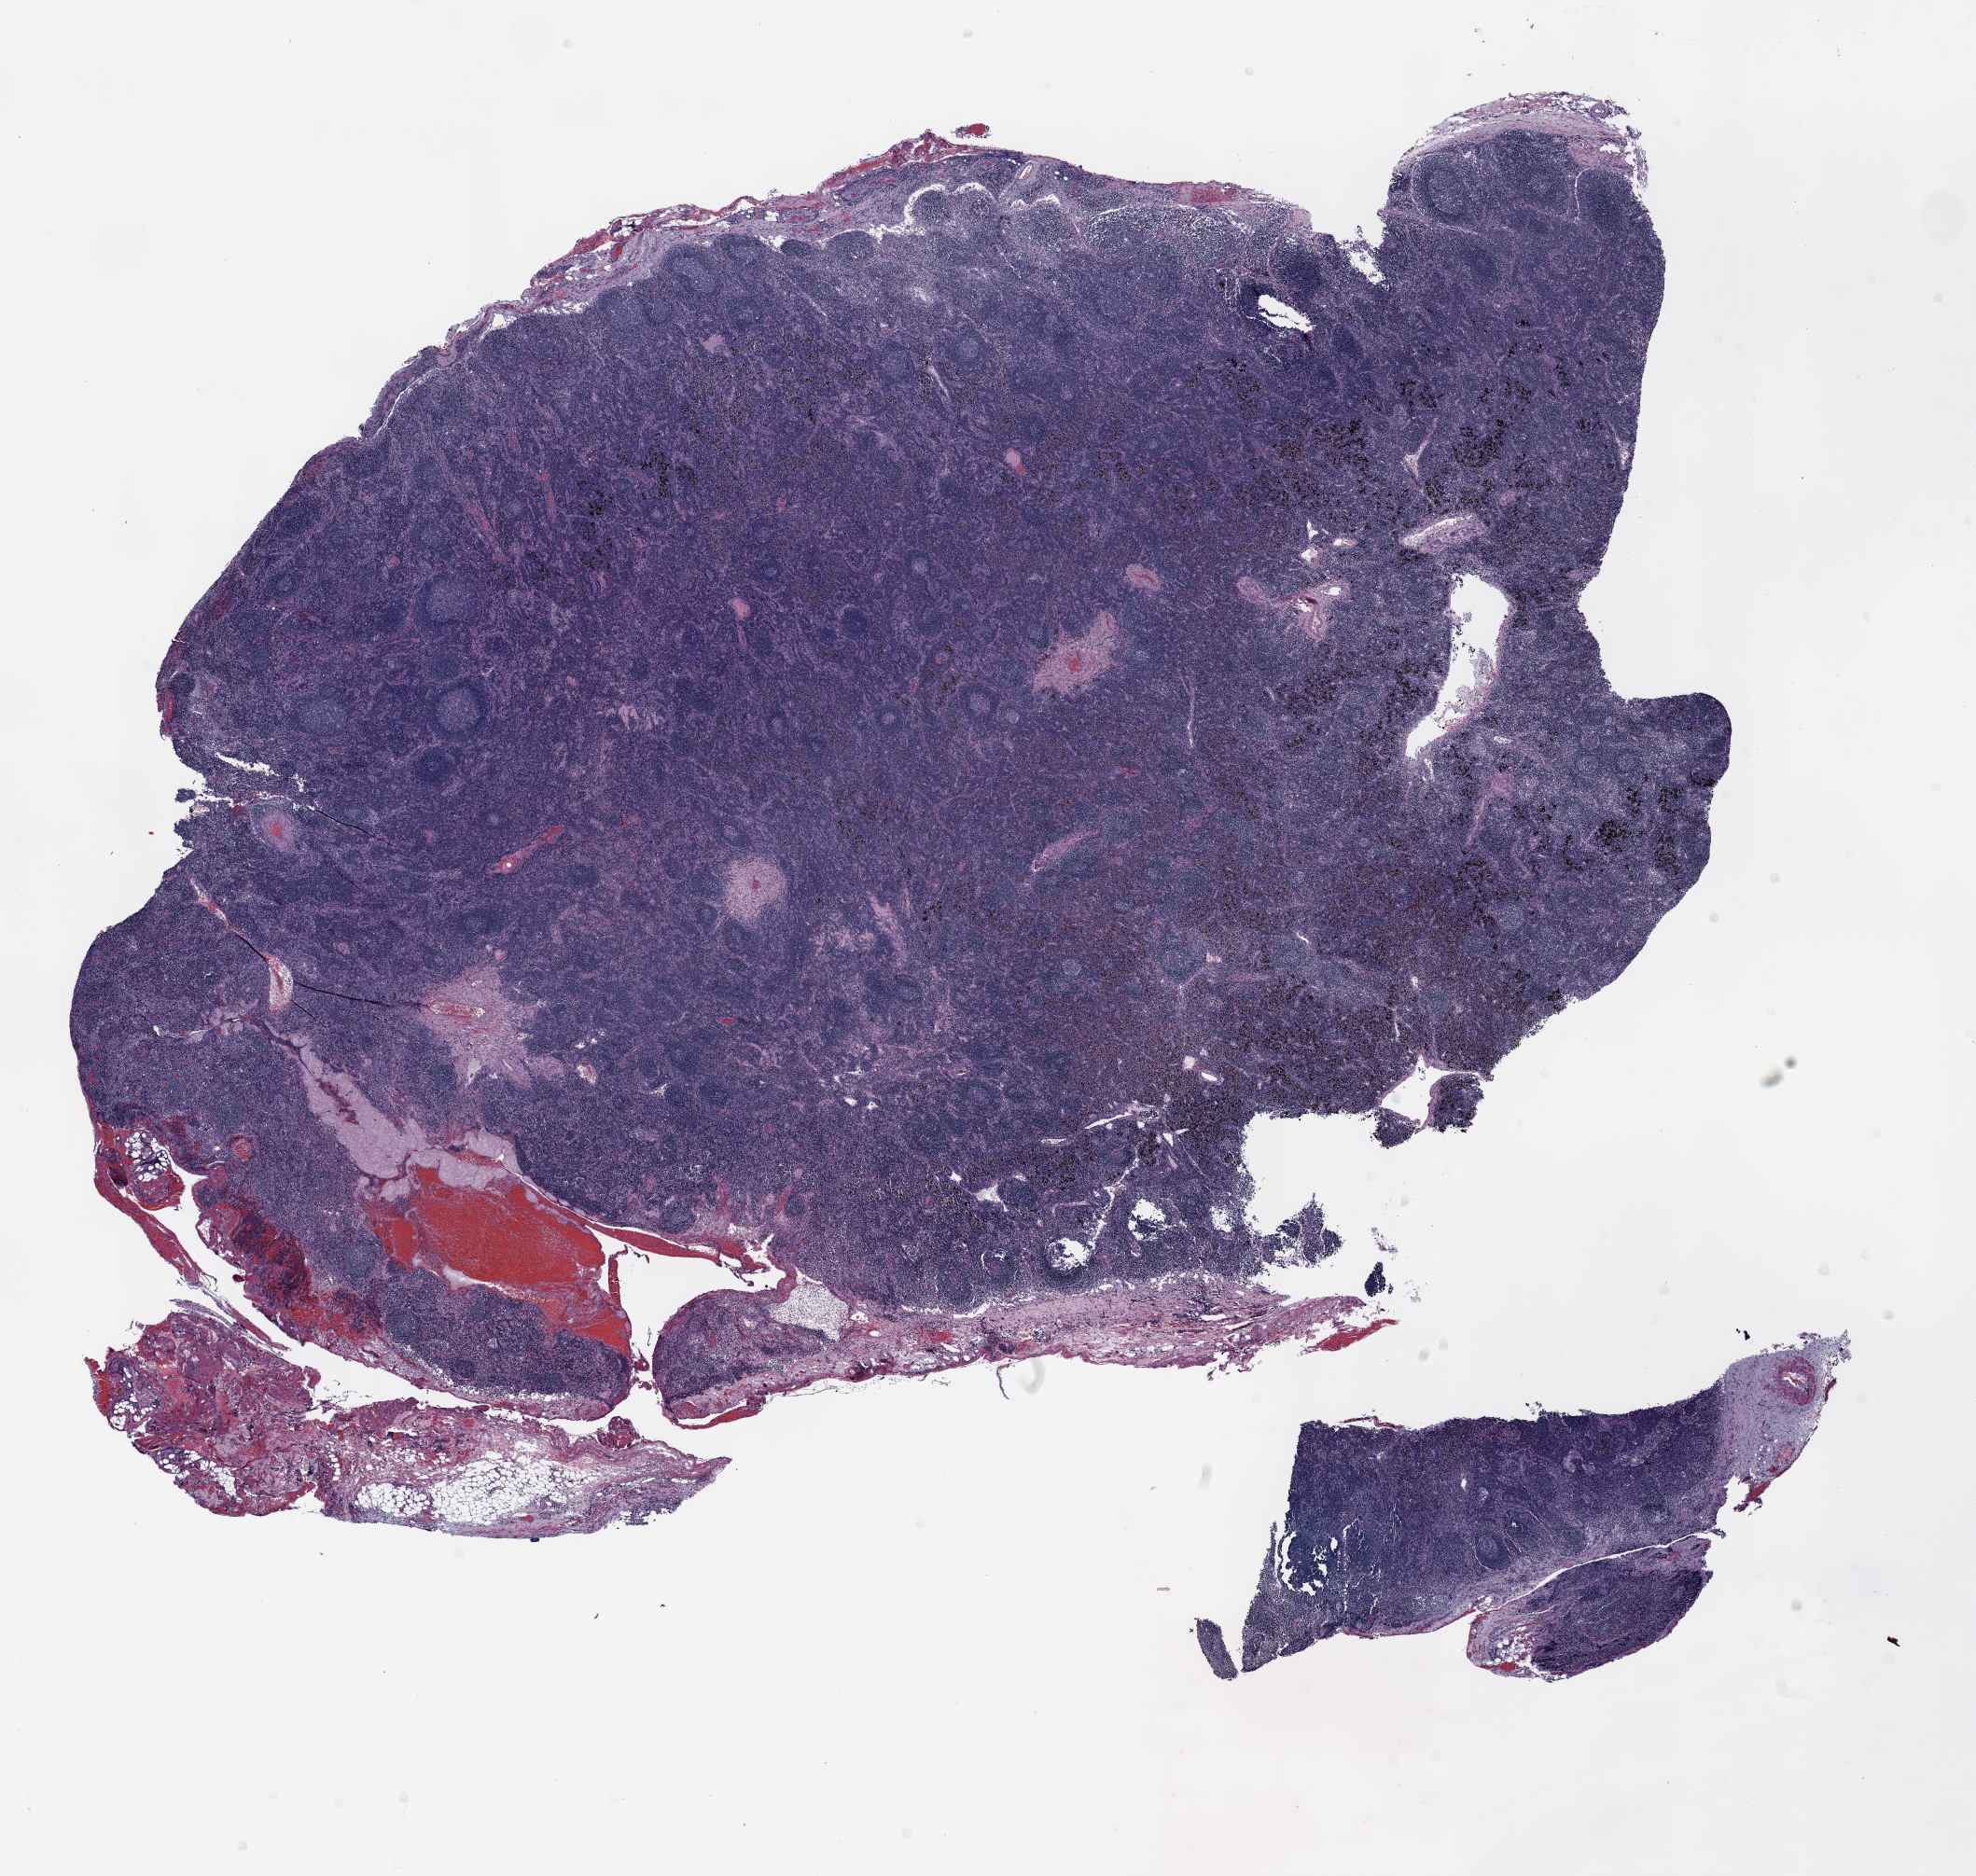
Whole-slide histology image, H&E — a low-resolution overview of the entire scanned area, about 17.0 x 16.2 mm (from a 20x scan). Formalin-fixed paraffin-embedded (FFPE) section. Lung. Male, age 55 at enrolment. Current smoker at enrolment. Grade: poorly differentiated (G3).
Primary tumour location (clinical record): right upper lobe. Tumour size (pathology): 115 mm. Stage (AJCC 6th edition): IIB. Participant's lung-cancer diagnosis: Adenocarcinoma, NOS (ICD-O-3 8140/3).